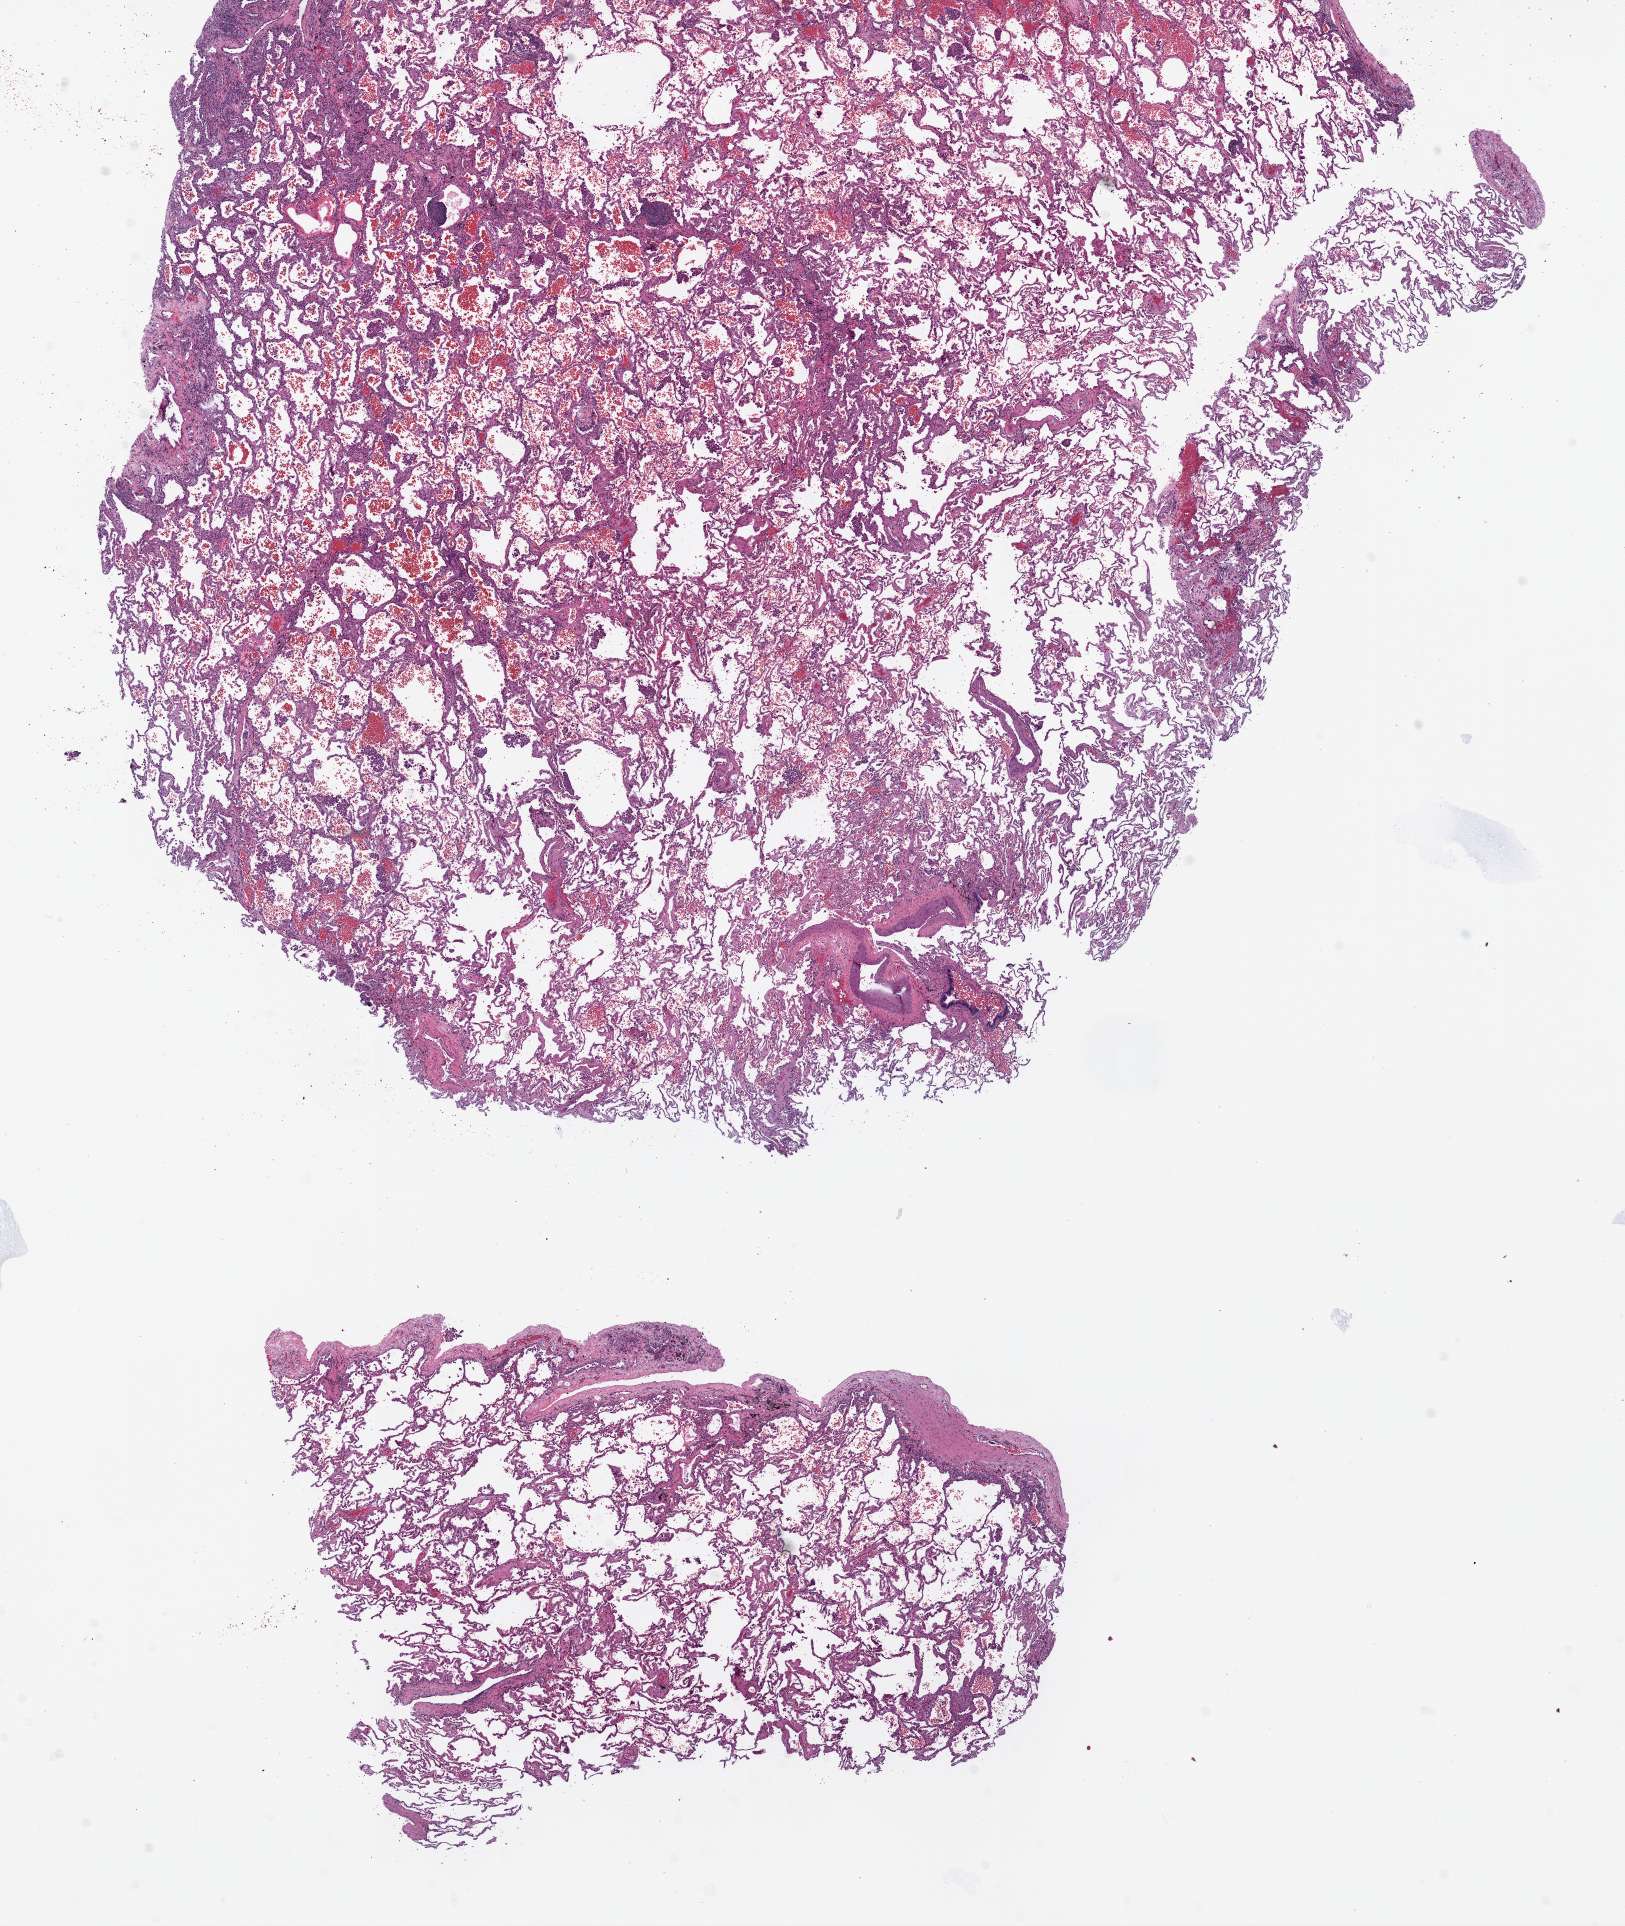
H&E whole-slide image — shown as a low-resolution overview of the whole scanned area (about 13.0 x 15.5 mm, acquisition: 20x scan). Frozen section from the top of the tissue portion. Solid tissue normal (non-tumour tissue) sample from the lung. Female patient; age at initial diagnosis 60 years.
This section: solid tissue normal (non-tumour) sample from the same patient. Patient diagnosis: Adenocarcinoma, NOS (upper lobe, lung).